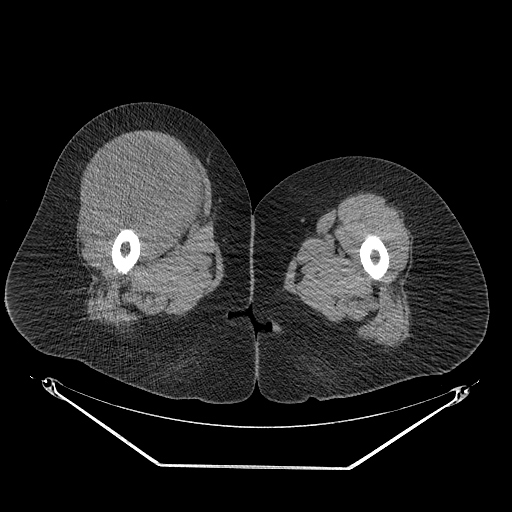
CT of an extremity soft-tissue mass (from a PET/CT study), one axial slice; slice 41 of 267 in the series (ordered by position); reconstruction kernel STANDARD; 140 kVp; soft-tissue window (W 400 / L 40 HU); 3.75 mm slice thickness; 512 × 512 image matrix. Female patient. From the clinical record (not read from this slice): histological type: malignant solitary fibrous tumor; grade: intermediate; site of the primary tumour: right thigh.
Structures marked on this image (expert contour drawn on MRI and transferred to this co-registered scan by the dataset authors):
- gross tumour volume including surrounding oedema: box from (x=80, y=137) to (x=209, y=234) px
- gross tumour volume (mass): (x=85, y=137)–(x=204, y=232)